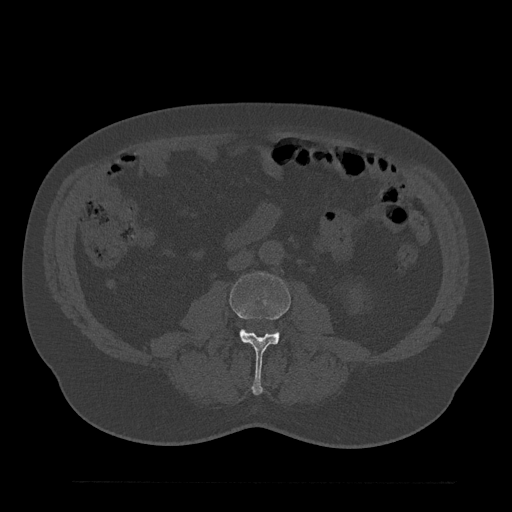
CT including the spine, one axial slice. Position 22 of 797 along the scan axis. Reconstruction kernel Br40s/3. 120 kVp. Bone window (W 1800 / L 400 HU). 512 × 512 image matrix, field of view 430 × 430 mm. Patient: male, 61 years. Case-level facts recorded for this patient, not image findings: primary cancer: prostate.
Structures marked on this image (semi-automatically segmented with operator editing):
- L3 vertebra: bounding box (x1, y1, x2, y2) in pixels: (230, 273, 291, 395)